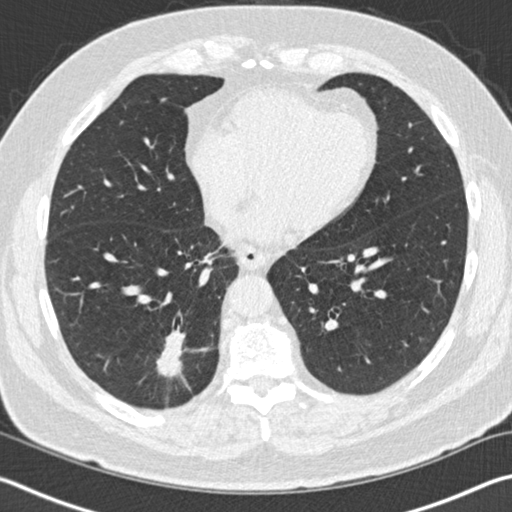
Low-dose screening chest CT, one axial slice; slice 41 of 141 in the series (ordered by position); 120 kVp; lung window (W 1500 / L -600 HU); 512 × 512 image matrix, field of view 344 × 344 mm.
Annotated regions visible in this slice (expert manual segmentation):
- lesion 1 (tumor, lower lobe of right lung): box from (x=156, y=329) to (x=185, y=378) px